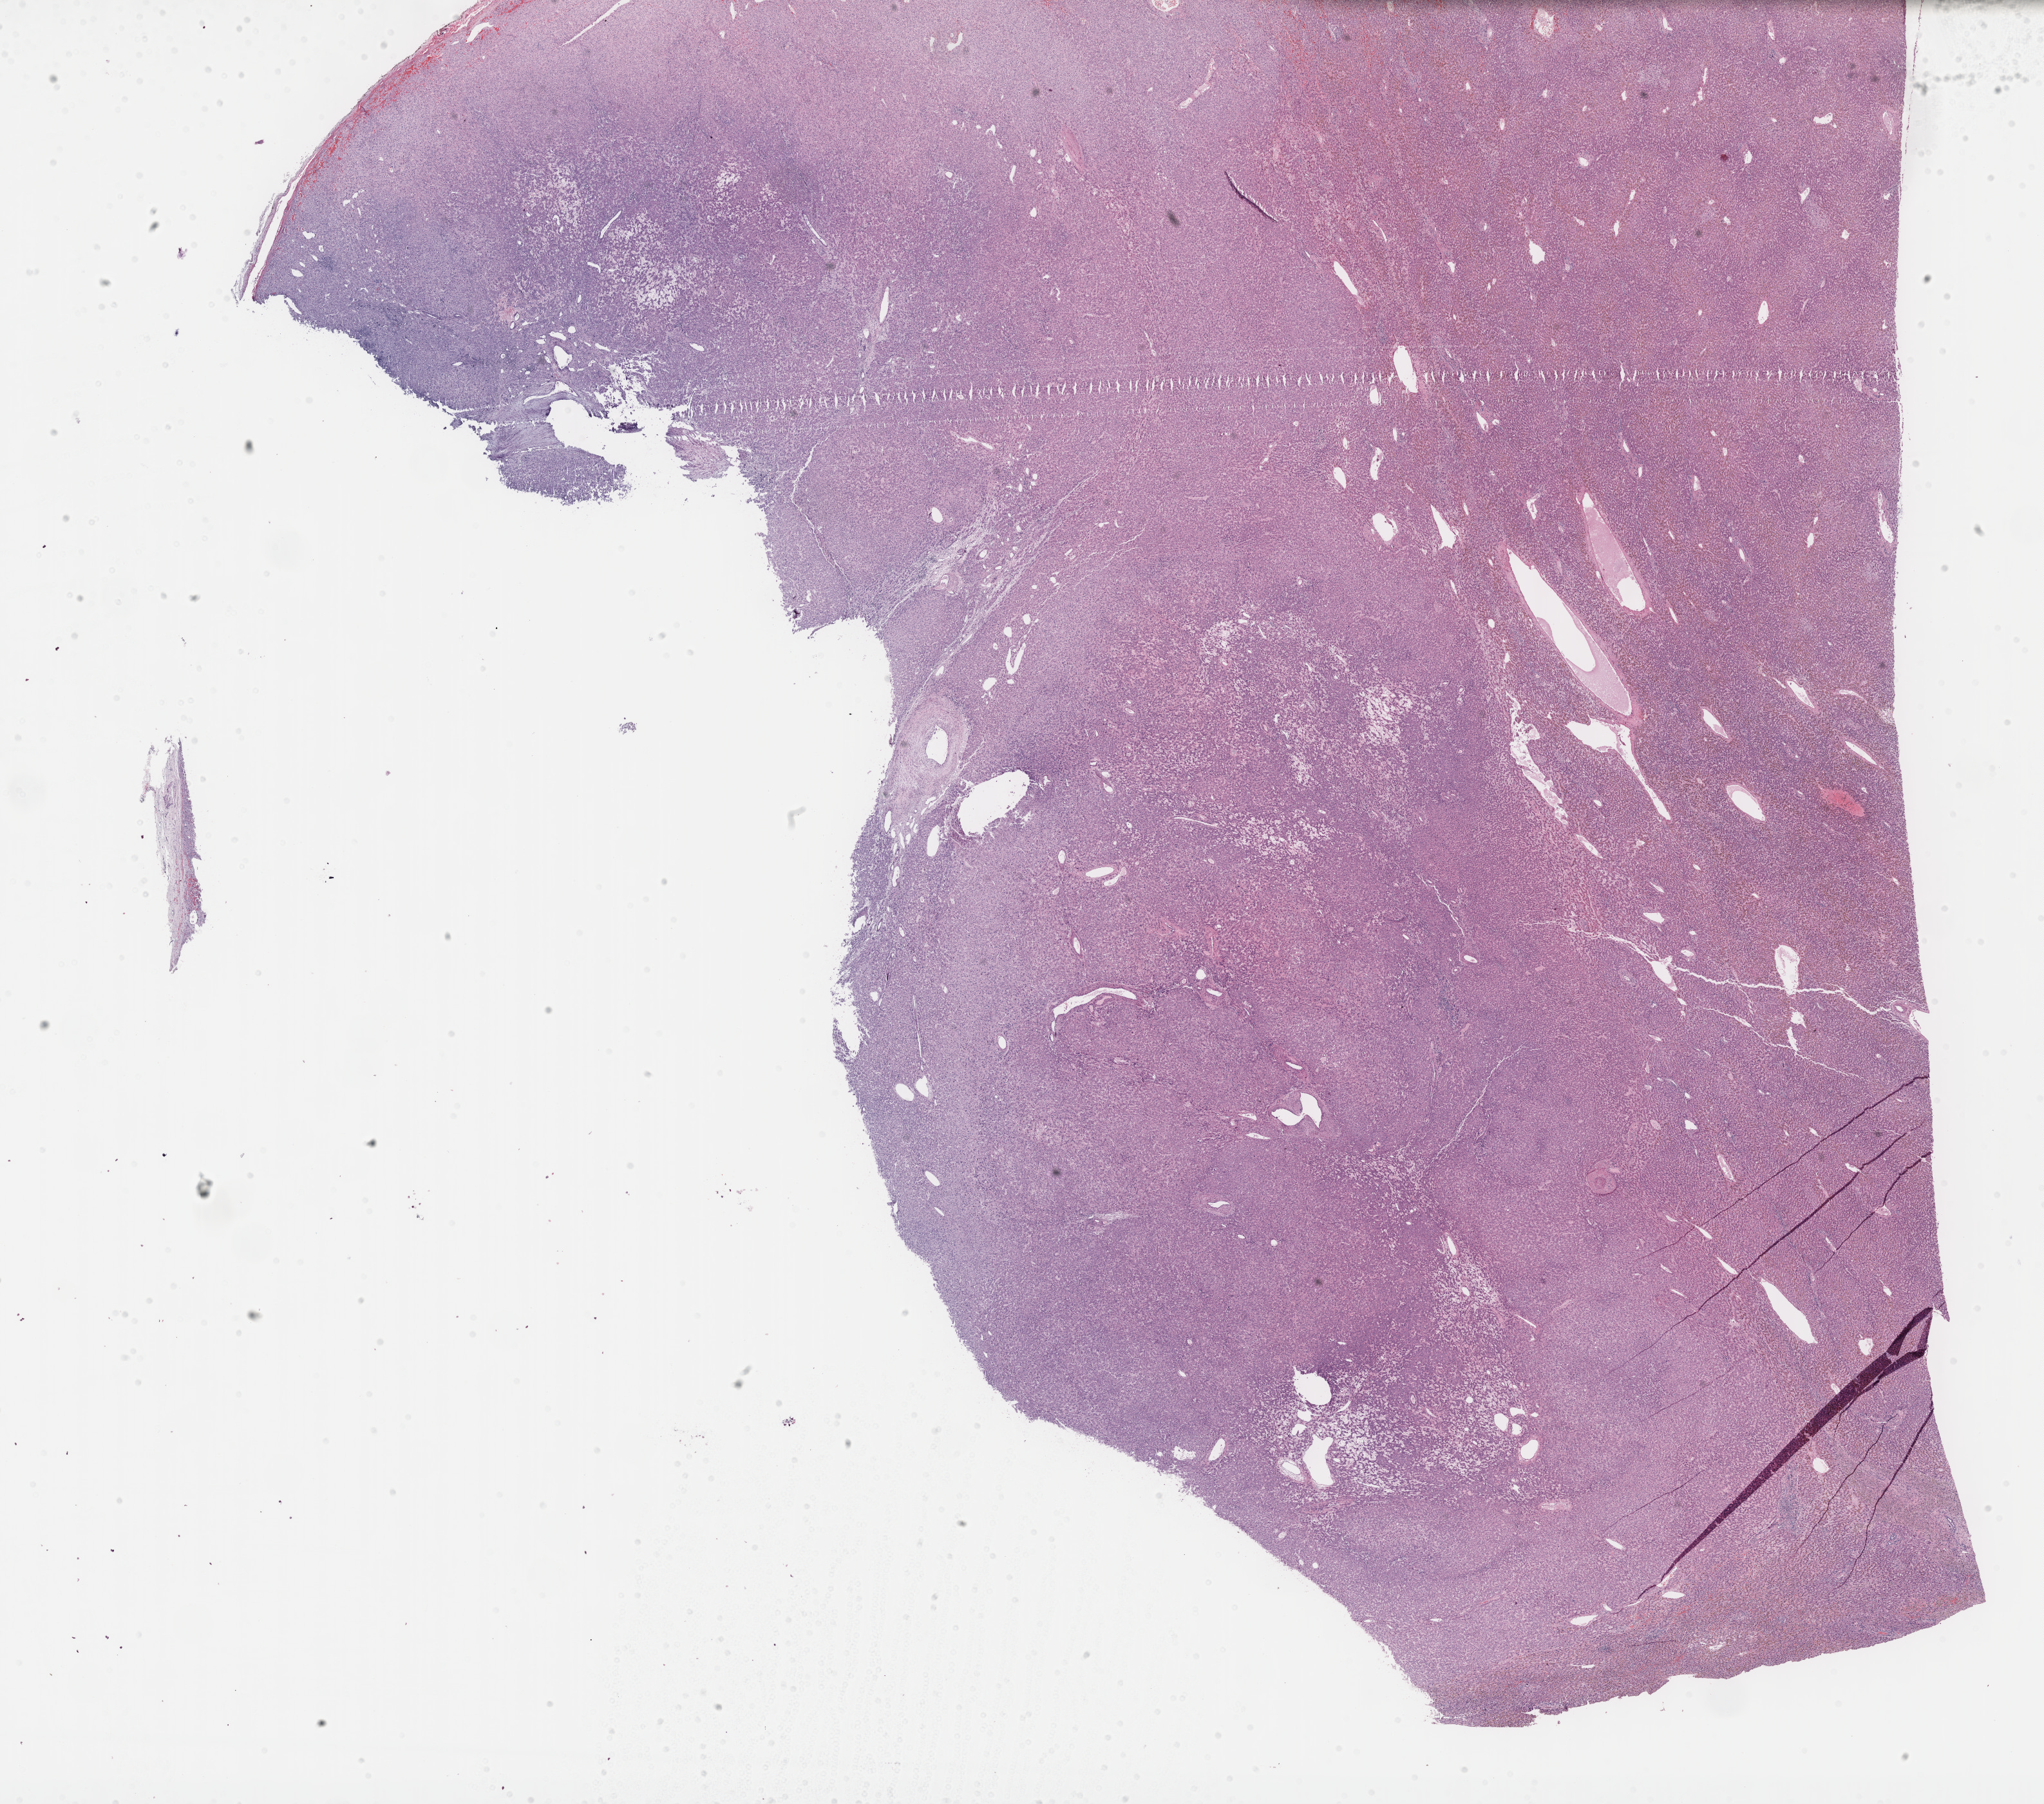
Whole-slide histology image, H&E-stained — low-resolution overview of the scanned area, about 25.7 x 22.7 mm; FFPE section; primary tumour sample from the liver. Patient: male, age at initial diagnosis 61 years. Histologic grade: G1 (well differentiated).
- AJCC pathologic stage: II
- diagnosis: Hepatocellular carcinoma, NOS